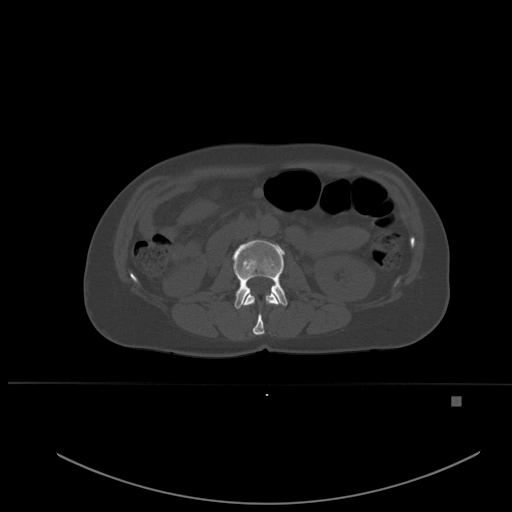
CT including the spine, one axial slice. Slice 220 of 651 in the series (ordered by position). Bone window (W 1800 / L 400 HU). 1.5 mm slice thickness. 512 × 512 image matrix. Patient: female, 49 years. From the clinical record (not read from this slice): primary cancer: breast.
Annotated regions visible in this slice (semi-automatic segmentation, software-assisted and operator-edited):
- L1 vertebra: box from (x=244, y=292) to (x=279, y=335) px
- L2 vertebra: (x=232, y=239)–(x=288, y=309)